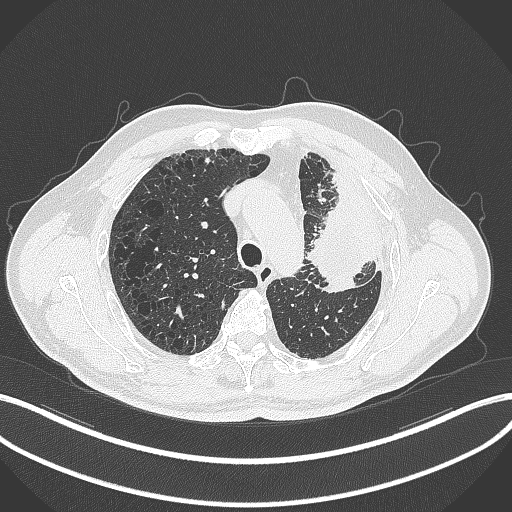
Chest CT, one axial slice; lung window (W 1500 / L -600 HU); 1 mm slice thickness; 512 × 512 image matrix. Male patient, age 68 years. From the clinical record (not read from this slice): clinical TNM (as recorded): T3 N3 M1.
Structures marked on this image (rectangle marked by the reading radiologist):
- lung tumour (recorded histology: adenocarcinoma): box from (x=308, y=190) to (x=368, y=295) px